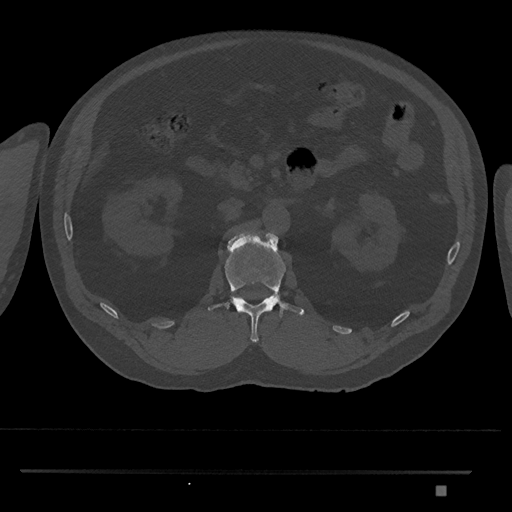
CT including the spine, one axial slice. Slice 814 of 1134 in the series (ordered by position). Reconstruction kernel Br40s/3. Bone window (W 1800 / L 400 HU). 512 × 512 image matrix, field of view 429 × 429 mm. Patient: male, 65 years. From the clinical record (not read from this slice): primary cancer: prostate.
Structures marked on this image (semi-automatically segmented with operator editing):
- L1 vertebra: bounding box <208,230,304,343> (left, top, right, bottom; pixels)